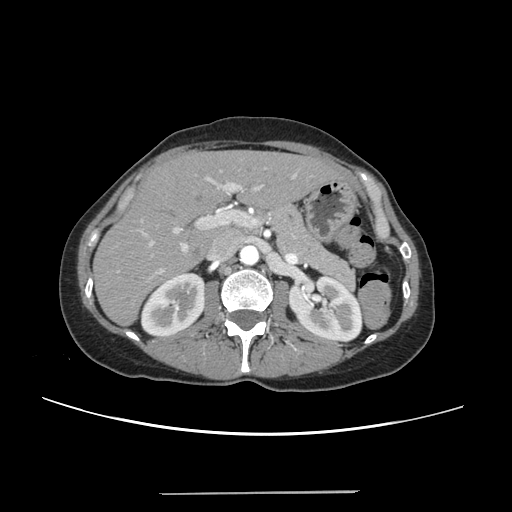
Contrast-enhanced abdominal CT, one axial slice. Position 138 of 240 along the scan axis. Intravenous contrast given. Soft-tissue window (W 400 / L 40 HU). 1.25 mm slice thickness. 512 × 512 image matrix. Female patient, age 60 years. From the clinical record (not read from this slice): diagnosis: colorectal cancer liver metastases, imaged before liver resection; multiple liver metastases: no.
Annotated regions visible in this slice (manually delineated by an expert):
- liver: bounding box <94,152,341,324> (left, top, right, bottom; pixels)
- planned liver remnant (the part of the liver to remain after resection): <94,152,341,324>
- portal vein (with intrahepatic branches): <117,171,297,276>